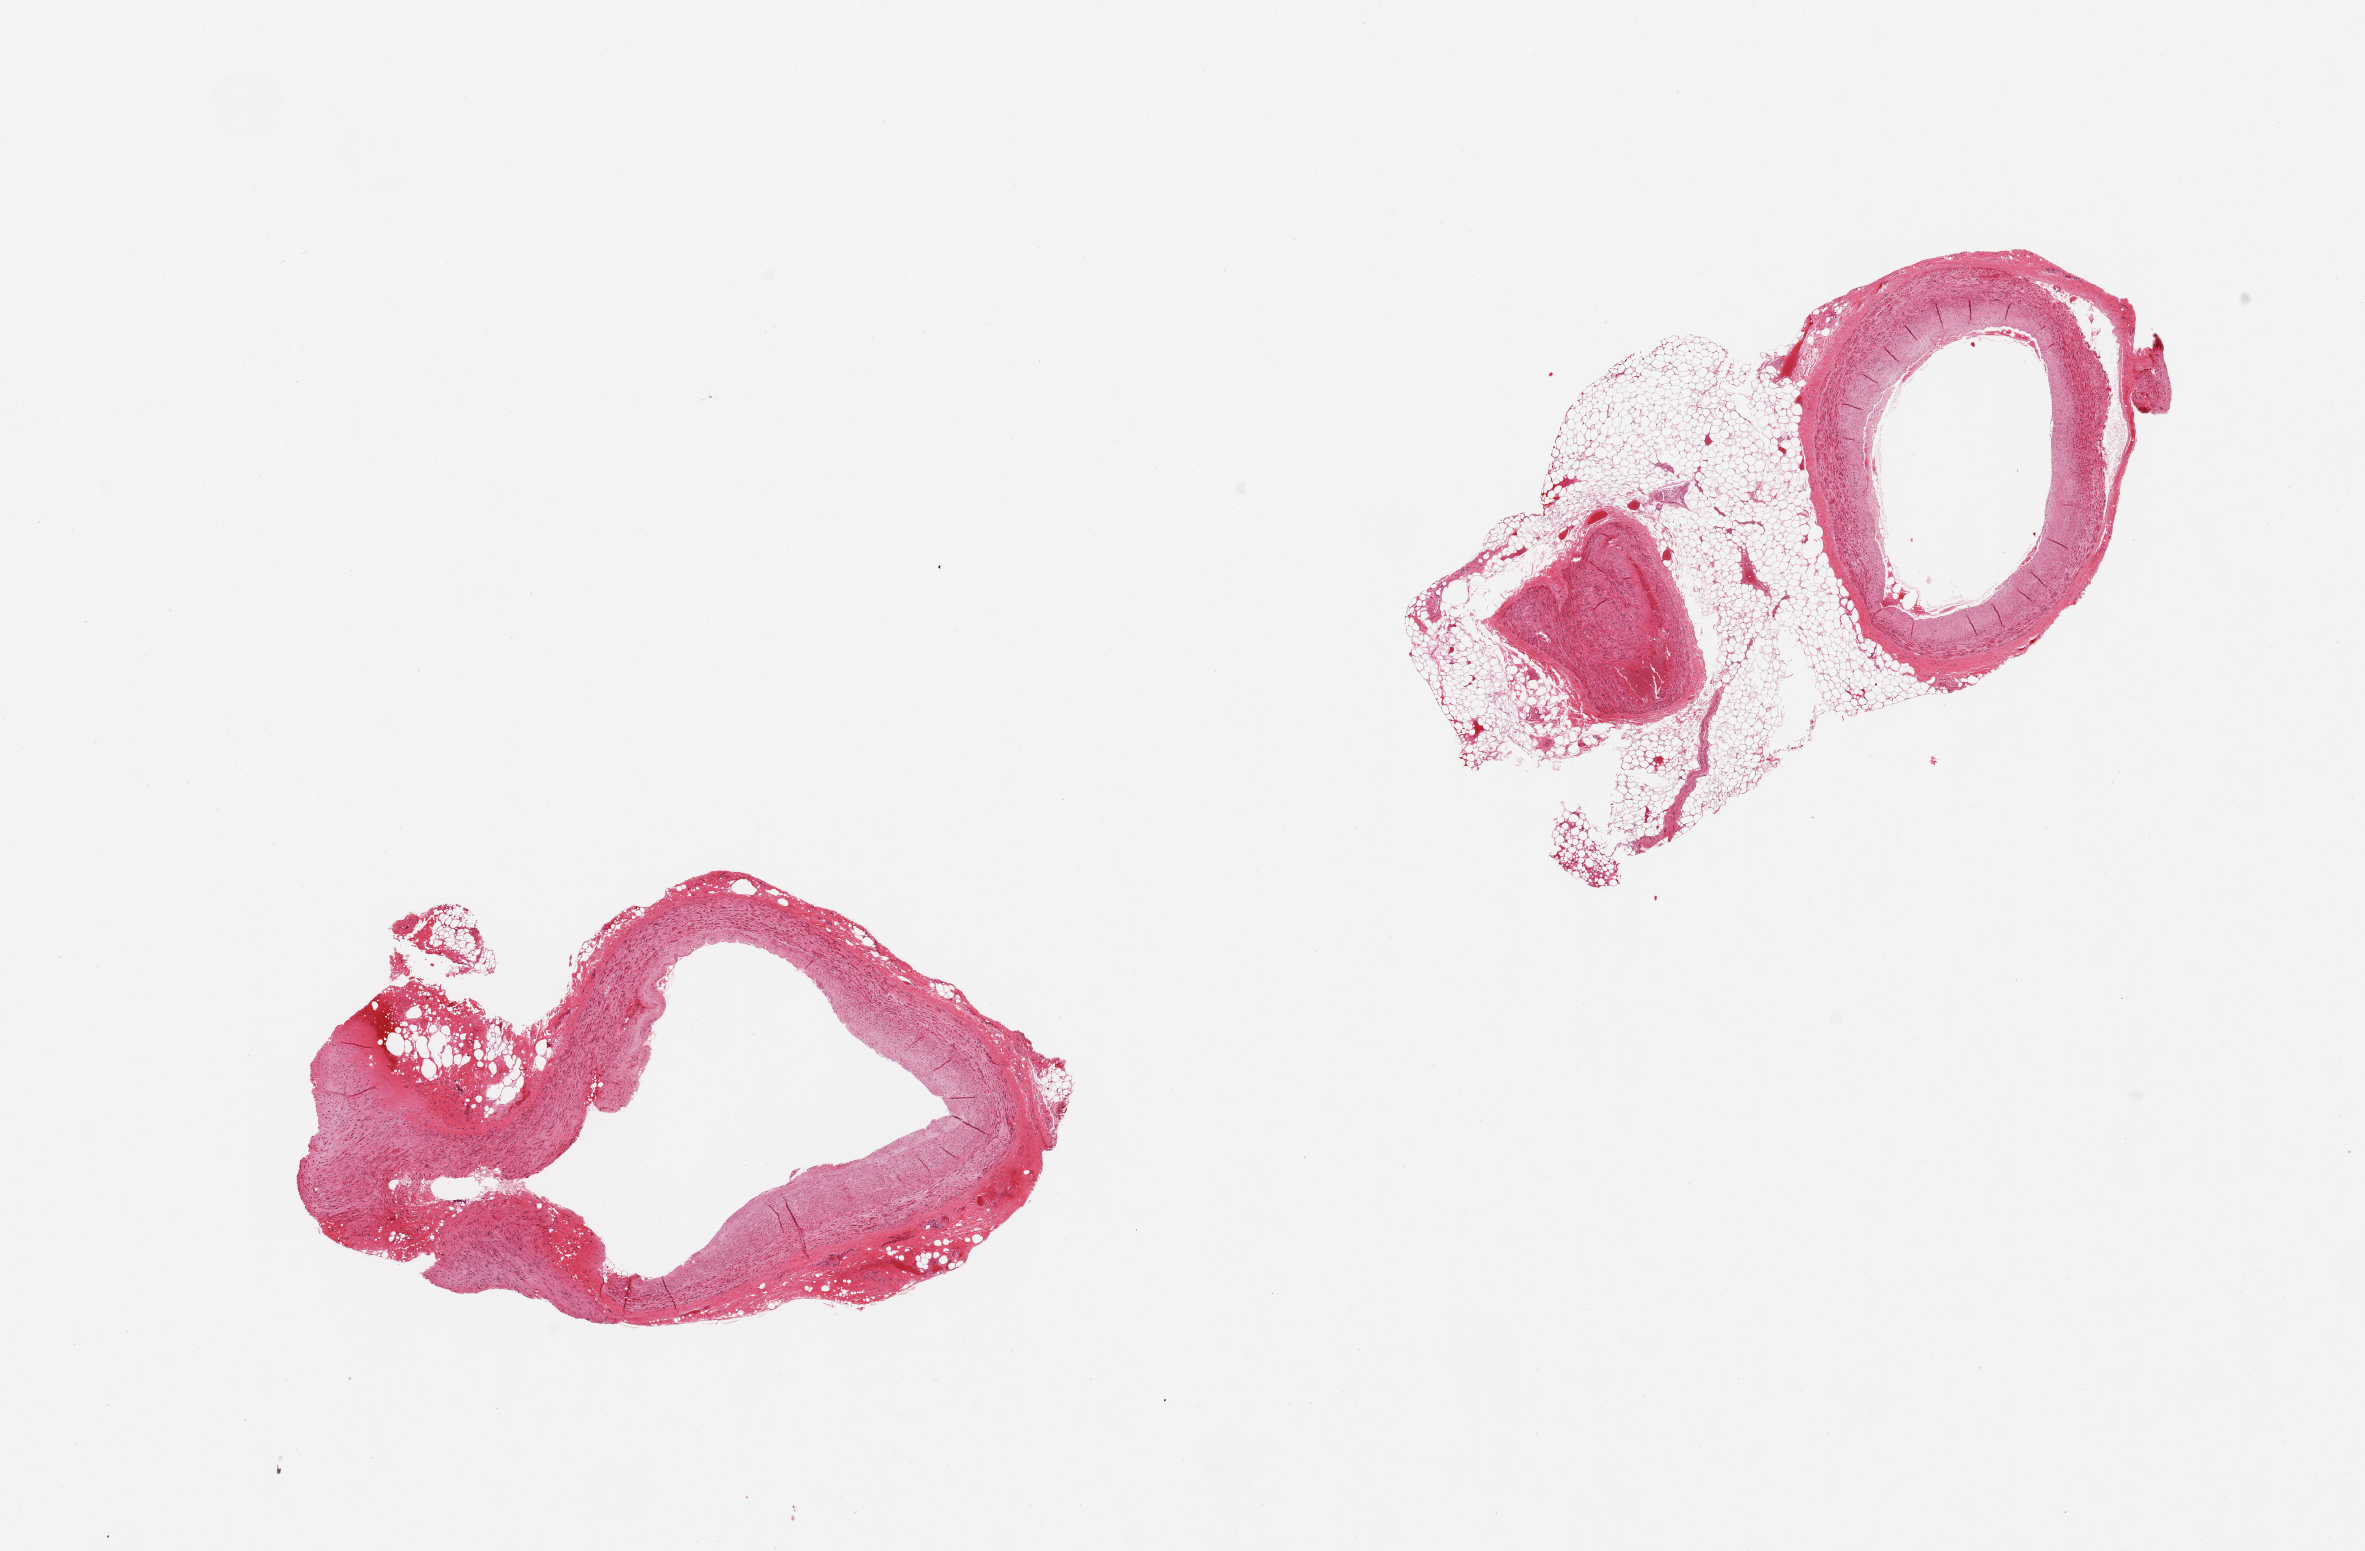
Whole-slide image, hematoxylin and eosin (H&E) stain, a low-resolution overview of the entire scanned area, about 18.7 x 12.3 mm (acquisition: 20x scan). PAXgene-fixed paraffin-embedded (PFPE) section. Sampled site (target tissue): coronary artery. Donor tissue sample. Donor sex: male.
Review note (as recorded): 2 pieces; 20 and 50% external fat.